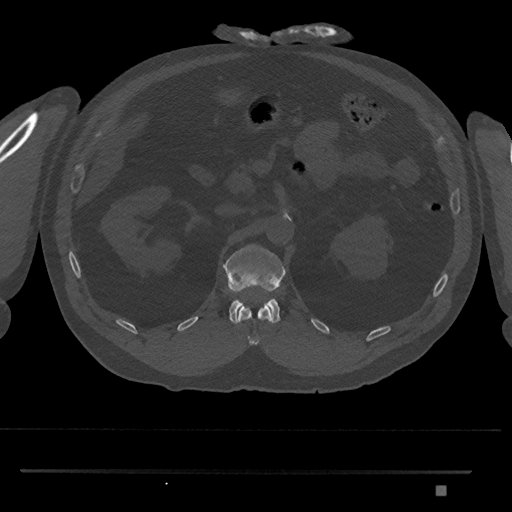
CT including the spine, one axial slice; slice 852 of 1134 in the series (ordered by position); 120 kVp; bone window (W 1800 / L 400 HU); 0.5 mm slice thickness; 512 × 512 image matrix. Patient: male, 65 years. Case-level facts recorded for this patient, not image findings: primary cancer: prostate.
Outlined on this slice (semi-automatic segmentation, software-assisted and operator-edited):
- L1 vertebra: box from (x=223, y=244) to (x=286, y=324) px
- T12 vertebra: (x=237, y=304)–(x=273, y=345)